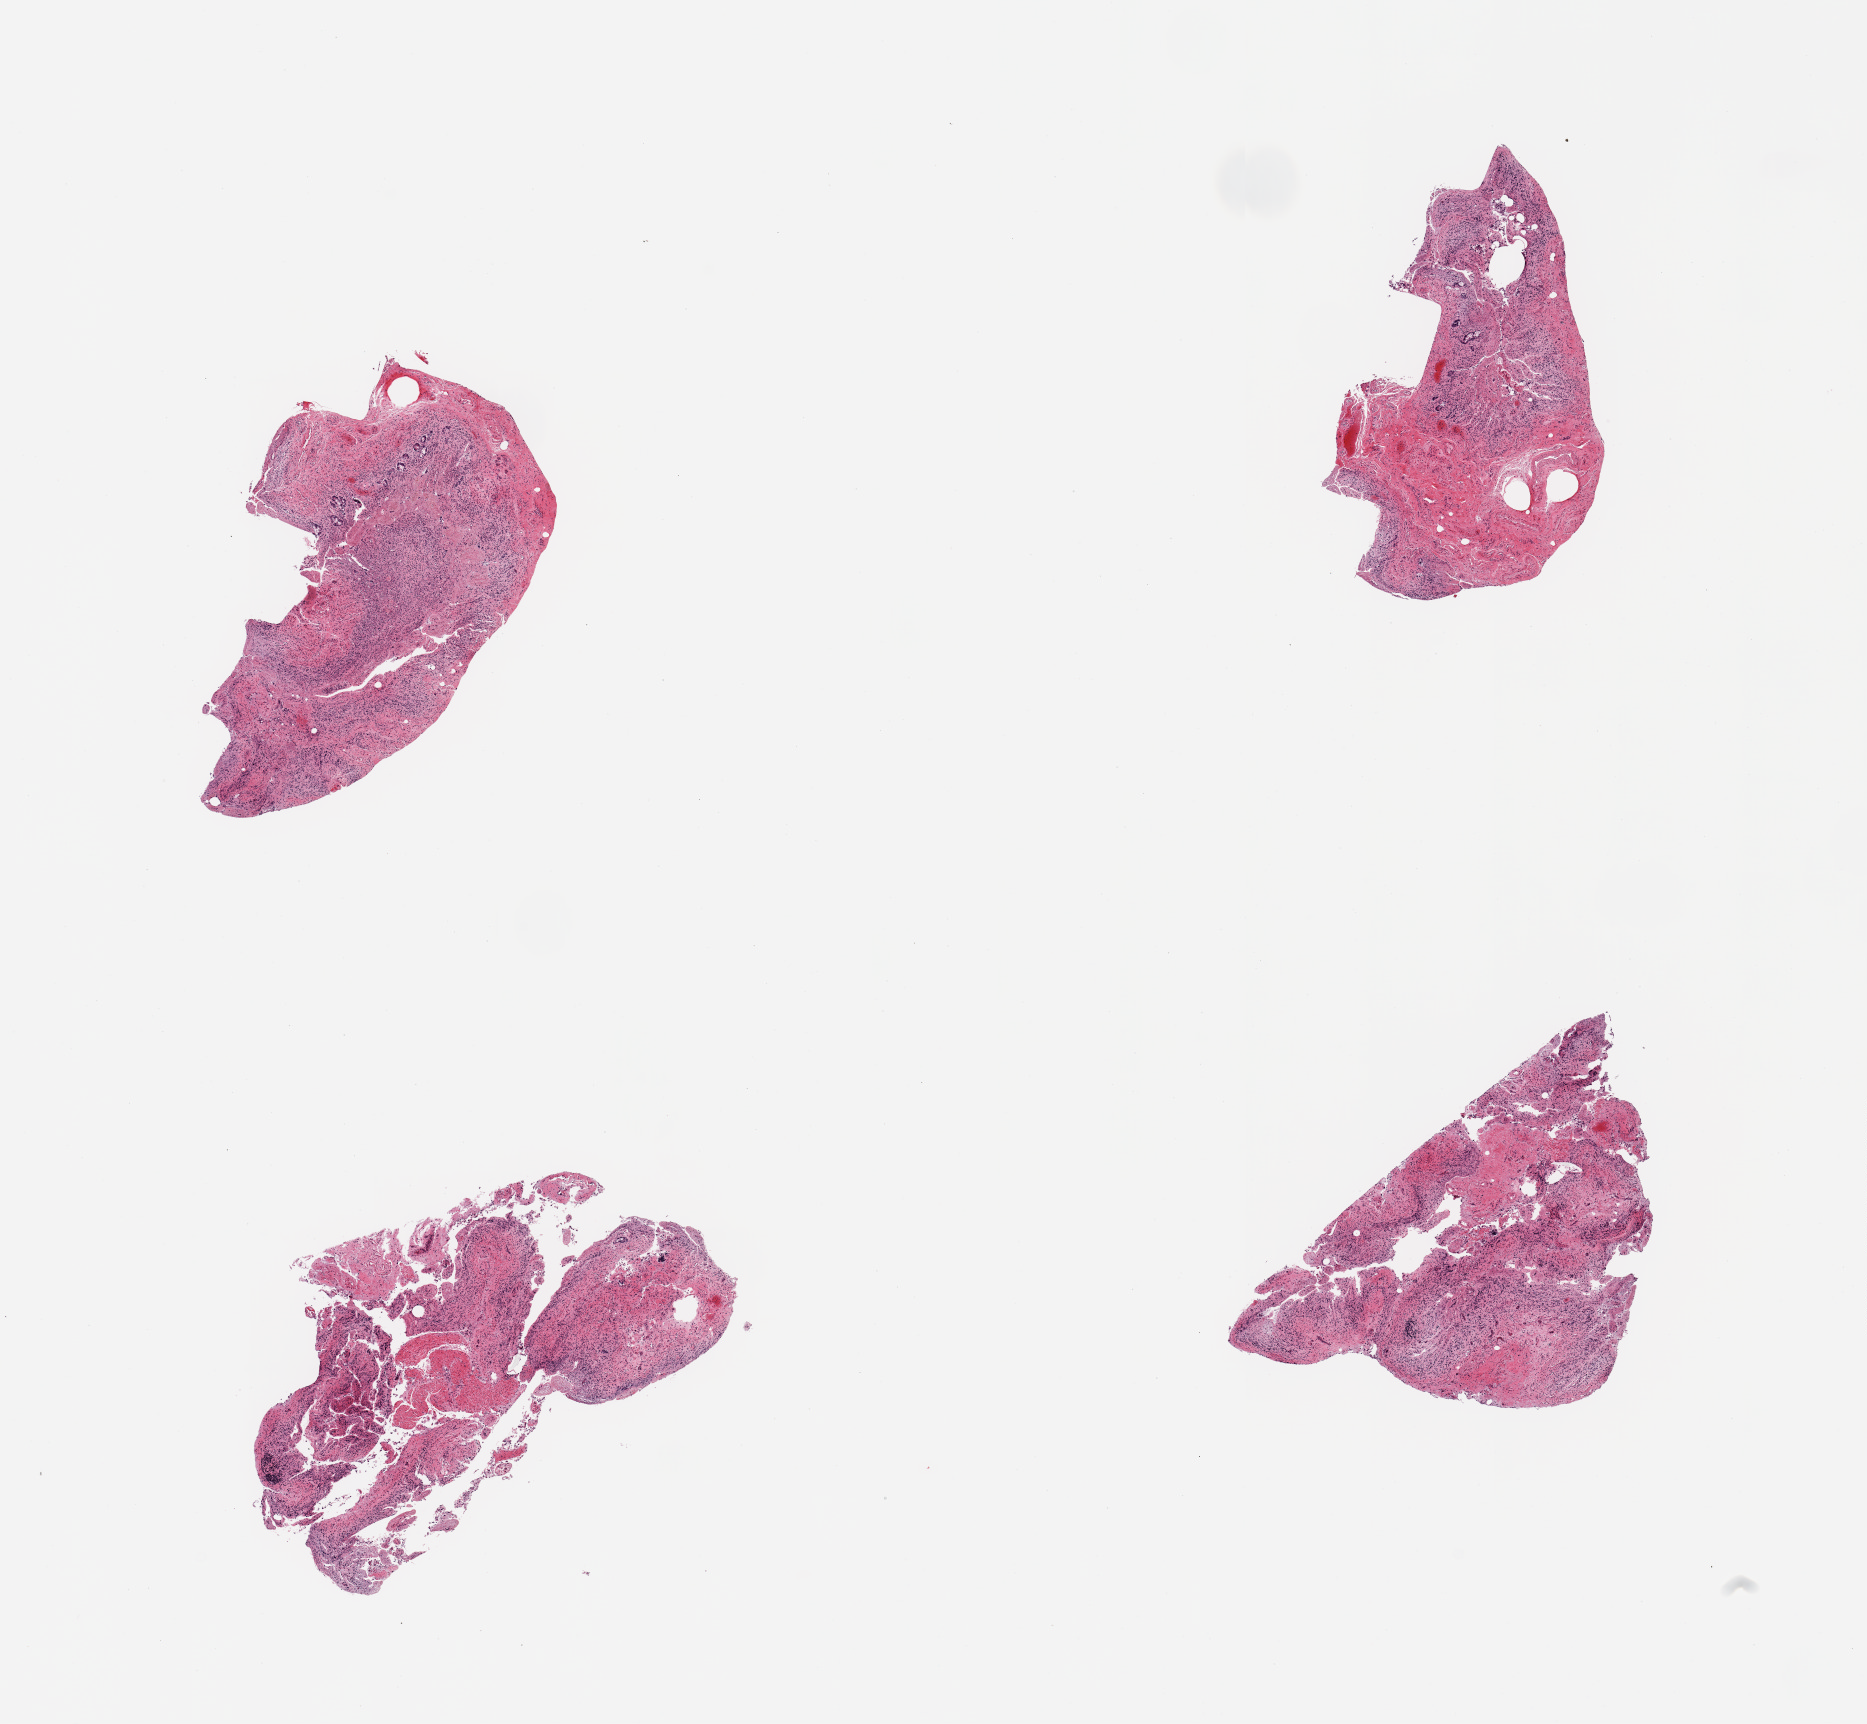
Haematoxylin and eosin whole-slide image — low-resolution overview of the scanned area, about 14.8 x 13.6 mm. PAXgene-fixed paraffin-embedded (PFPE) section. Section of ileum (target tissue). Donor tissue sample. Donor: female.
Review note (as recorded): 4 pieces, totally autolyzed, inadquate lymphoid aggregates to warrant analysis.